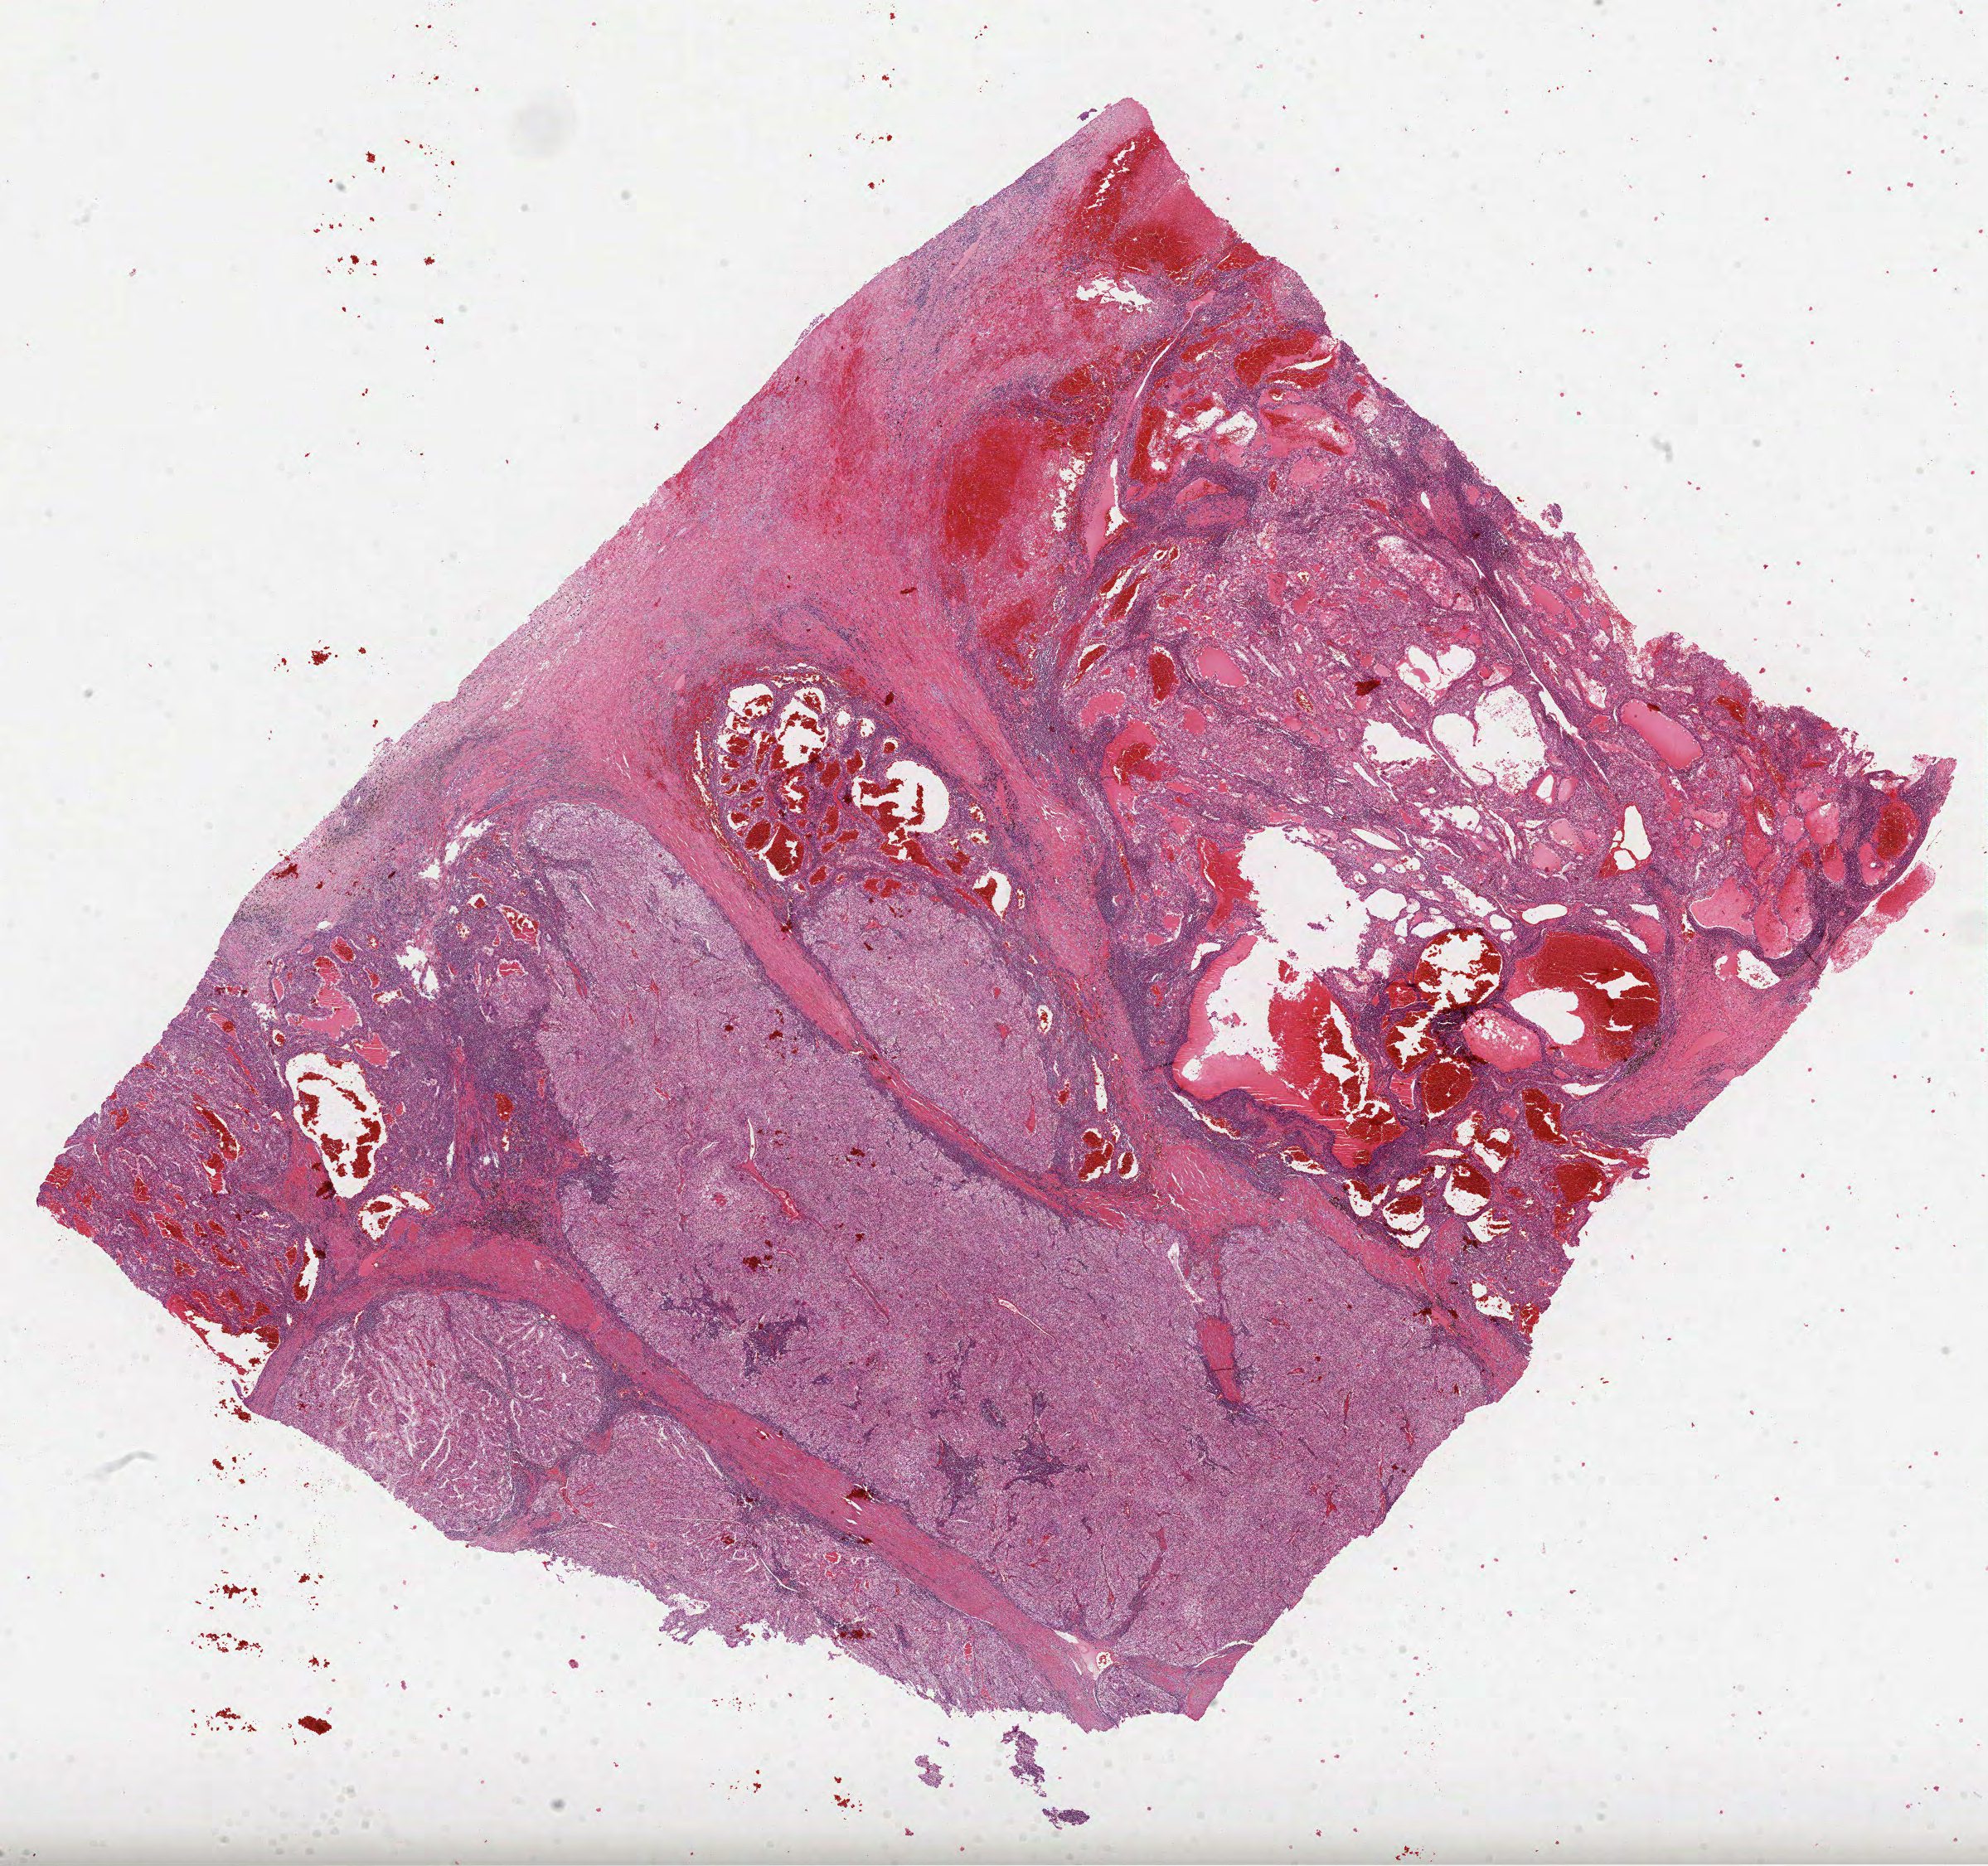
Whole-slide histology image, H&E-stained — whole scanned area (about 19.3 x 18.2 mm) shown as a low-resolution overview. Formalin-fixed paraffin-embedded (FFPE) diagnostic section. Kidney, primary tumour sample. Male, age 65 years at initial diagnosis. Histologic grade: G4 (undifferentiated).
Laterality: left. AJCC pathologic stage: III. Diagnosis: Clear cell adenocarcinoma, NOS.